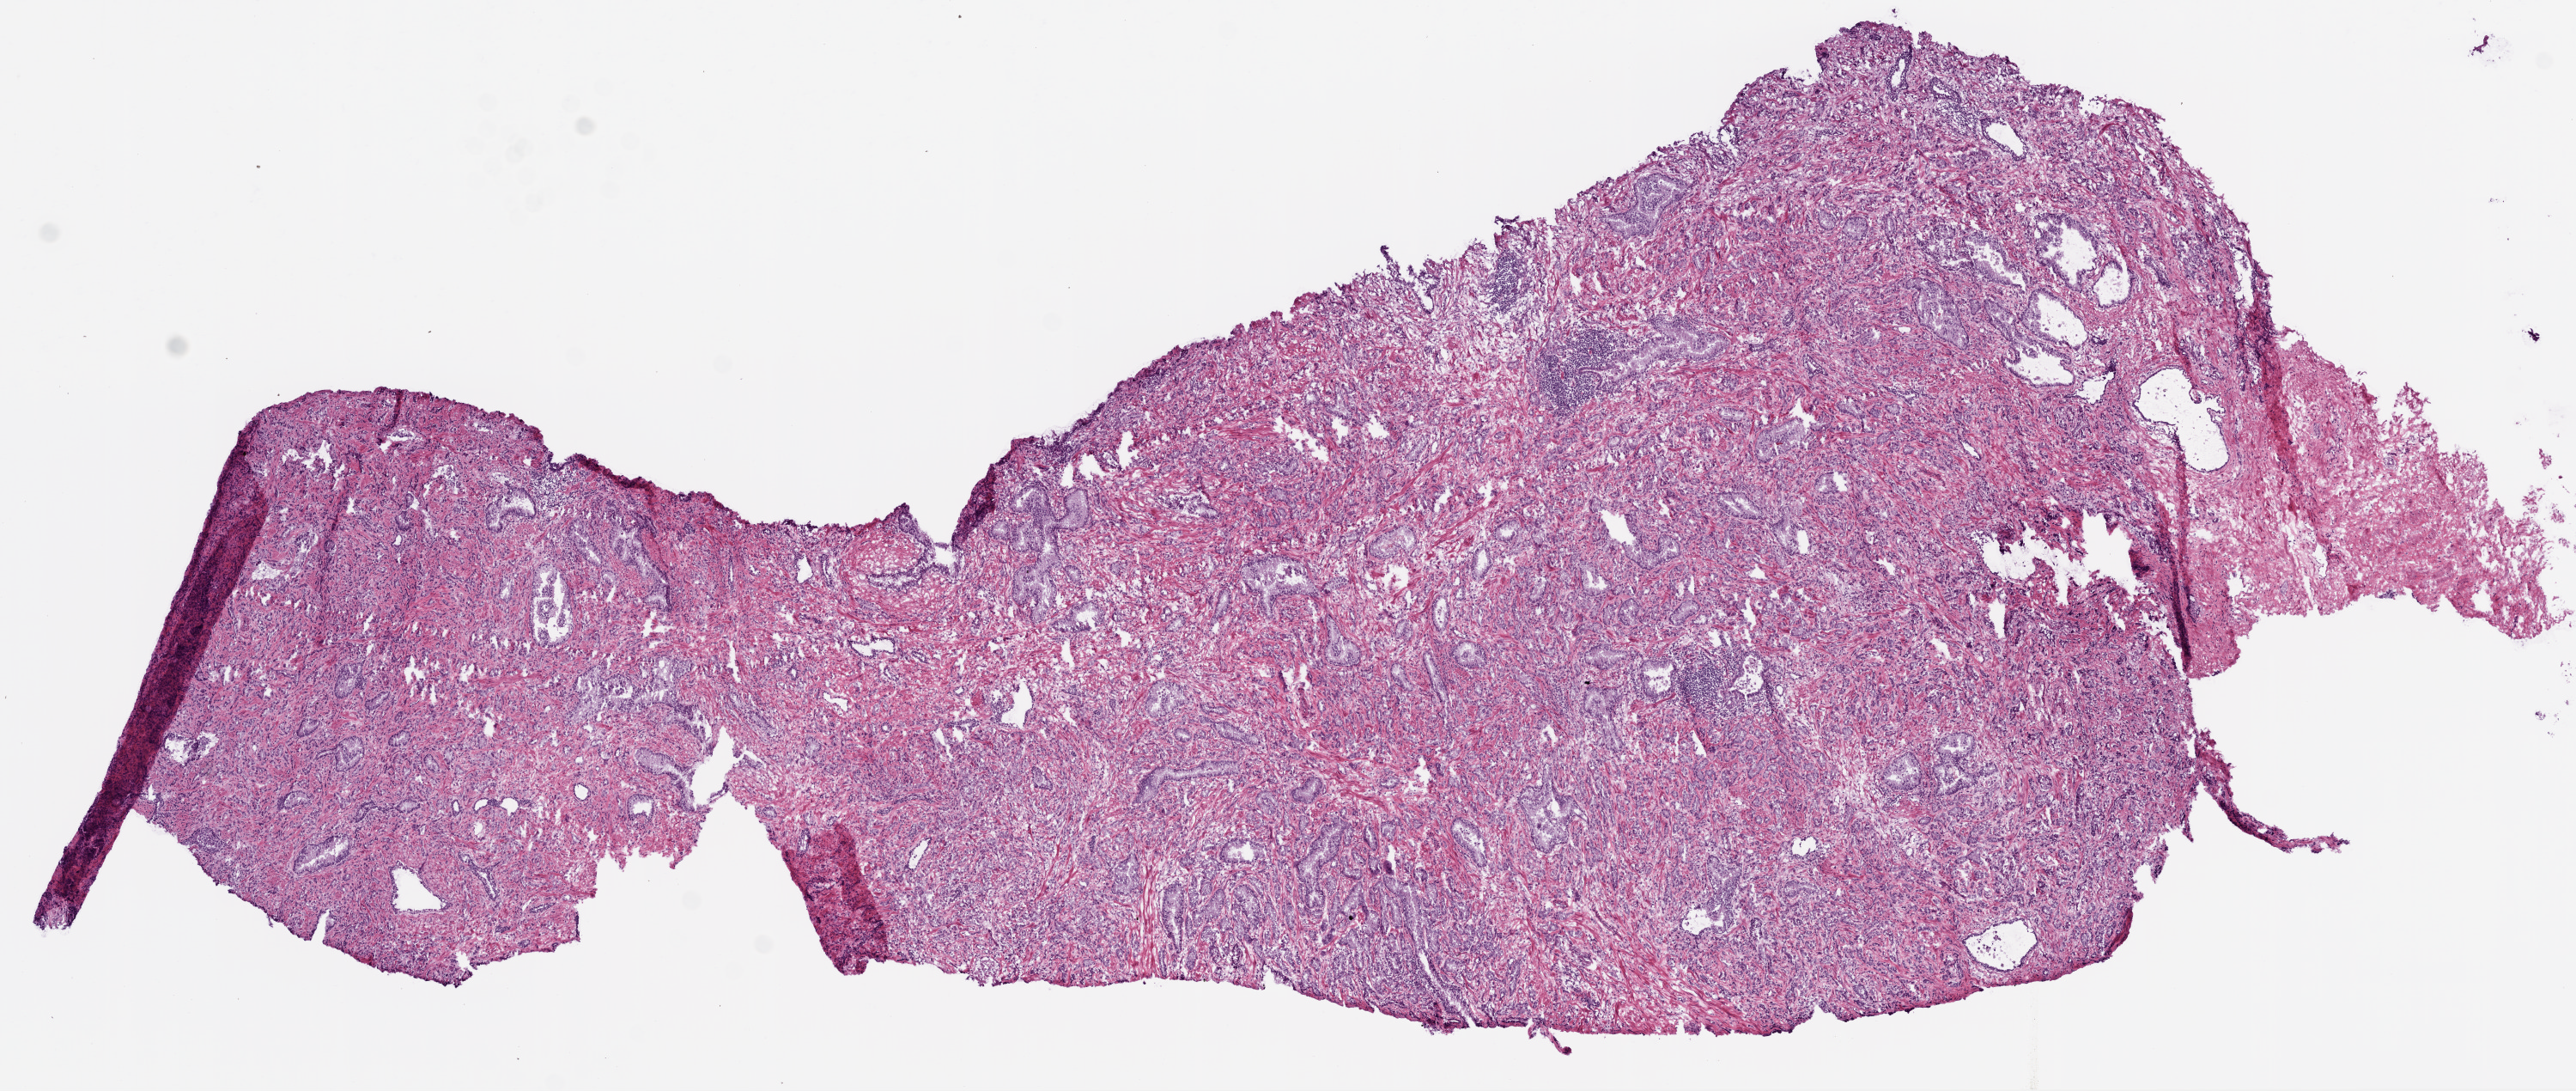
Whole-slide histology image, H&E-stained, a low-resolution overview of the entire scanned area, about 12.0 x 5.1 mm (acquisition: 20x scan), frozen section from the top of the tissue portion, prostate, primary tumour sample. Male, age 57 years at initial diagnosis.
Pathologic diagnosis: Acinar cell carcinoma (prostate gland).